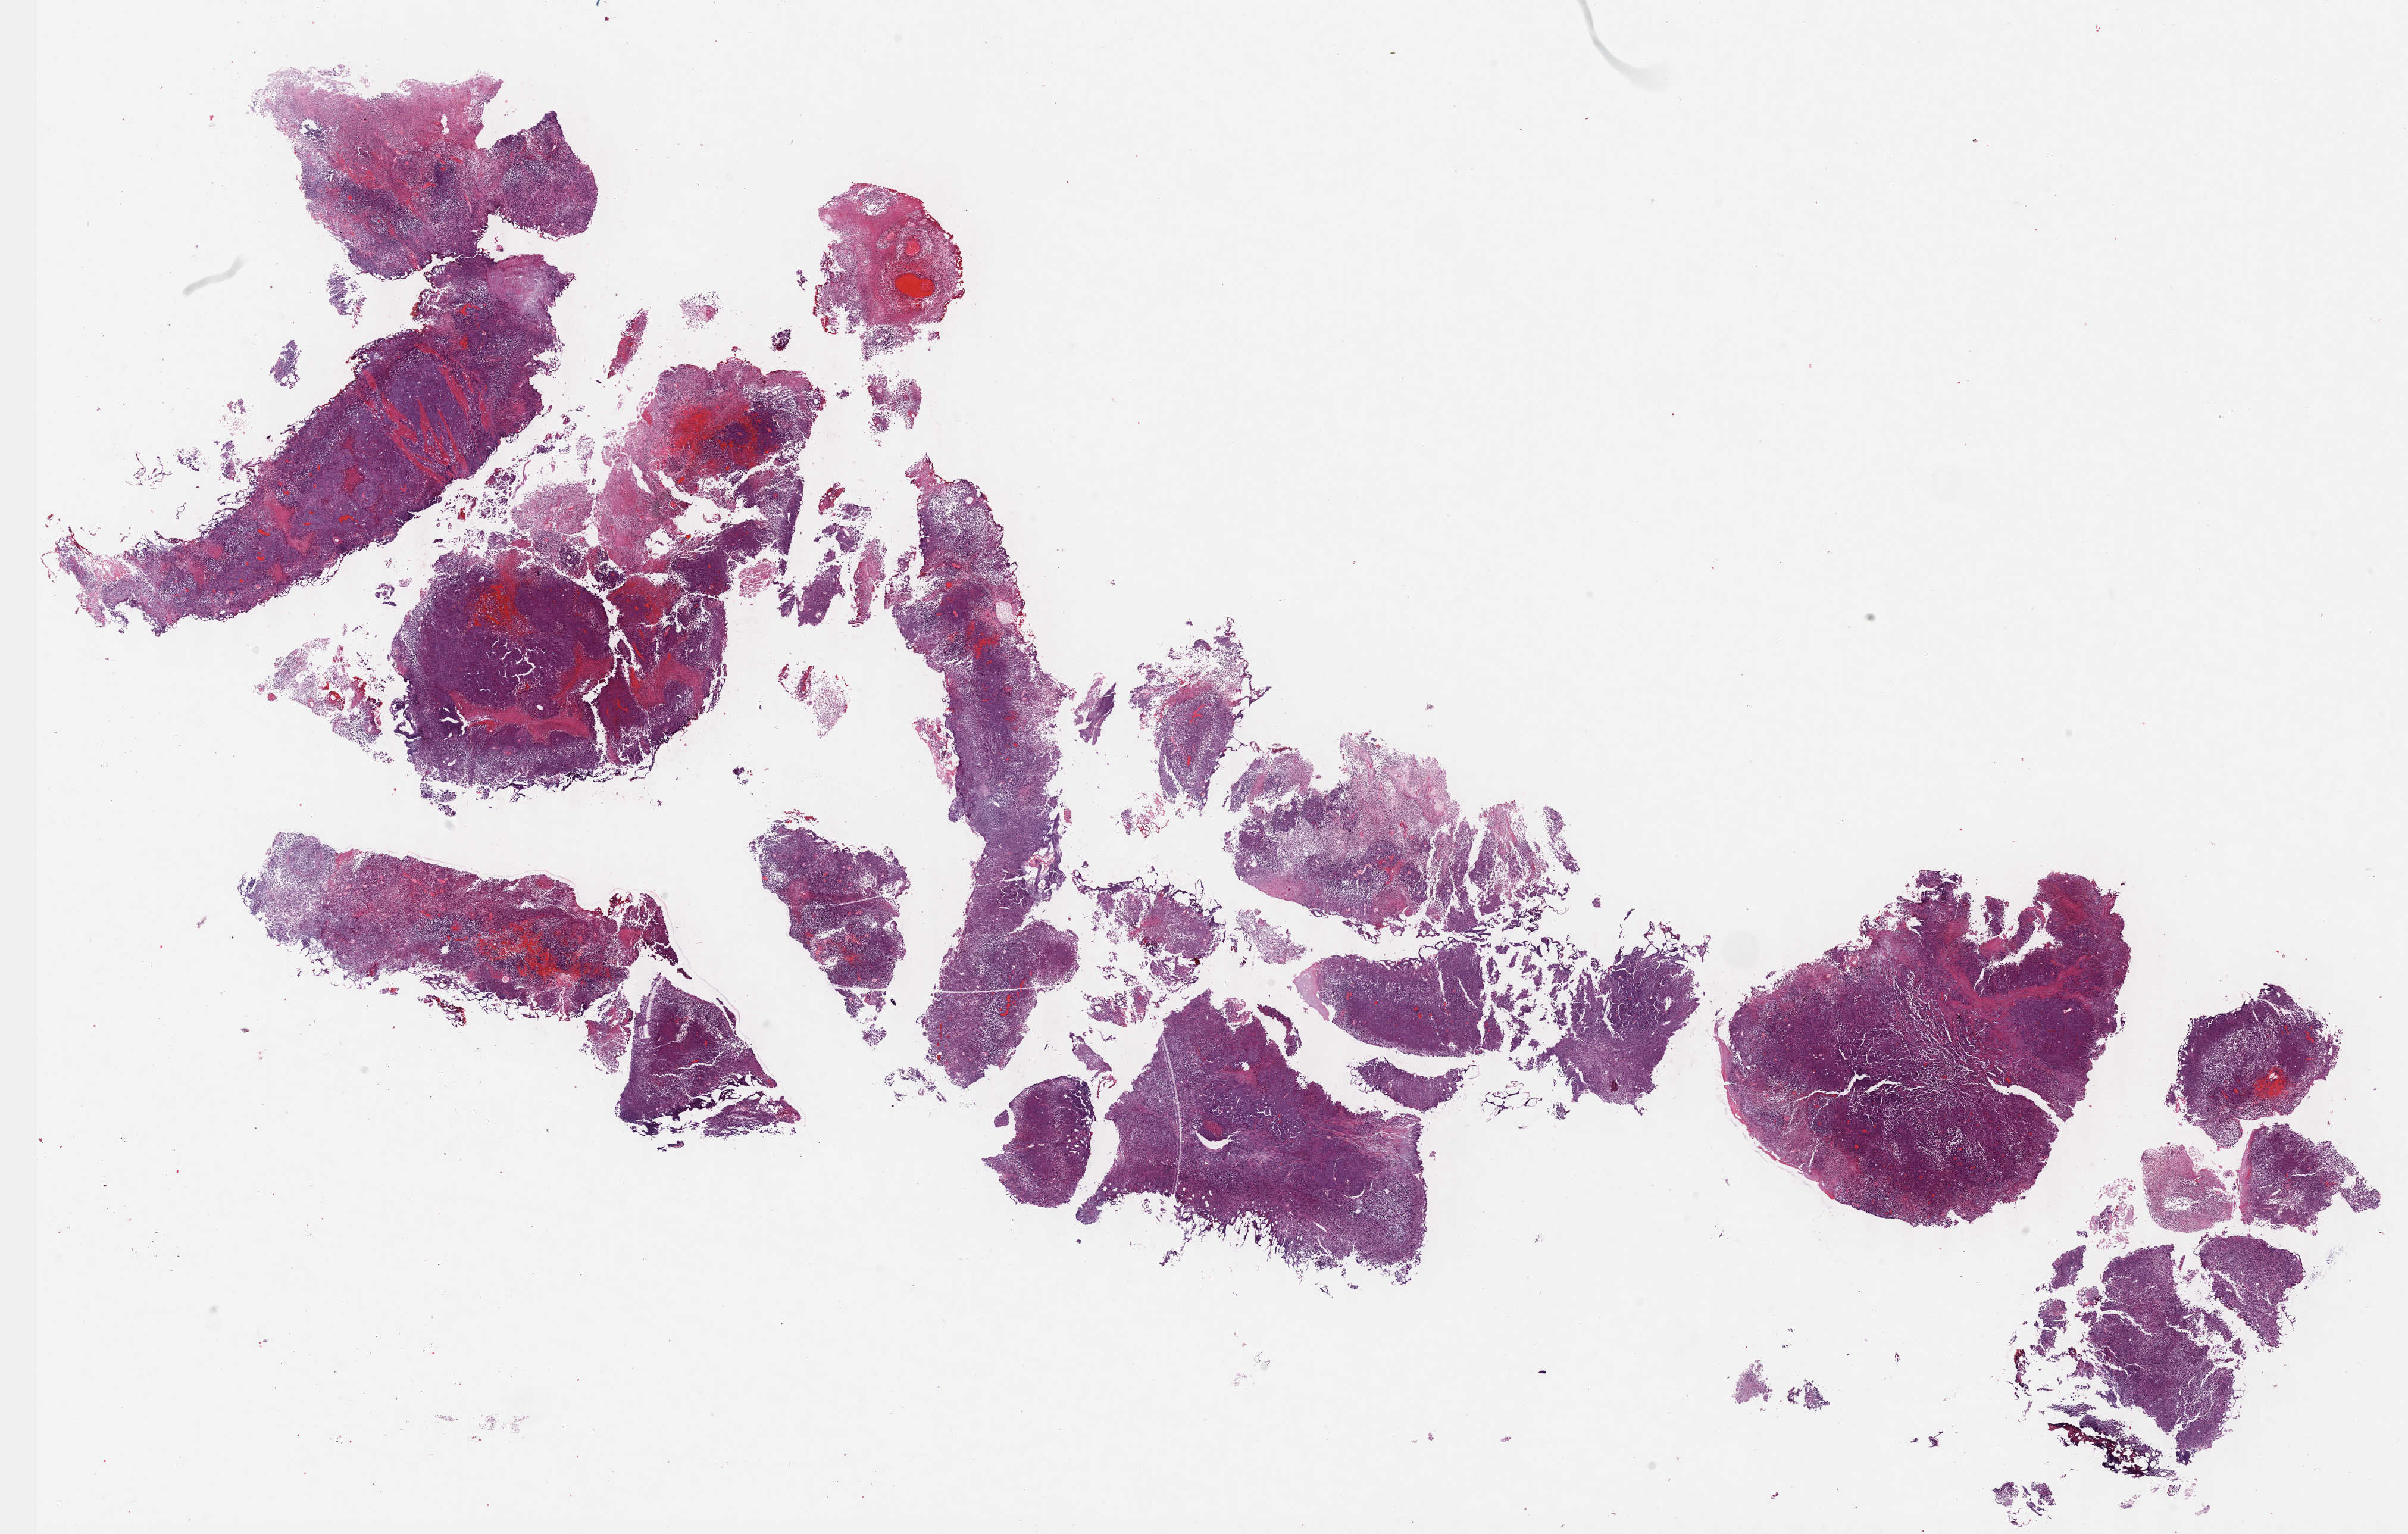
H&E-stained whole-slide image — low-resolution overview of the scanned area, about 32.7 x 20.8 mm (acquisition: 40x scan). FFPE section. Primary tumour sample from the bladder. Male, age 49 years at initial diagnosis. Histologic grade: high grade.
Pathologic diagnosis: Transitional cell carcinoma (lateral wall of bladder). AJCC pathologic stage: III (7th edition).